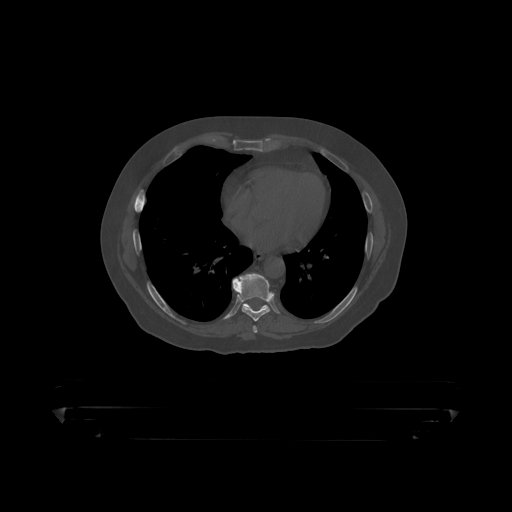
CT including the spine, one axial slice. Position 254 of 390 along the scan axis. 120 kVp. Bone window (W 1800 / L 400 HU). 512 × 512 image matrix, field of view 650 × 650 mm. Patient: male, 60 years. From the clinical record (not read from this slice): primary cancer: prostate.
Structures marked on this image (semi-automatically segmented with operator editing):
- T8 vertebra: box from (x=233, y=273) to (x=273, y=319) px
- T9 vertebra: (x=234, y=278)–(x=268, y=309)